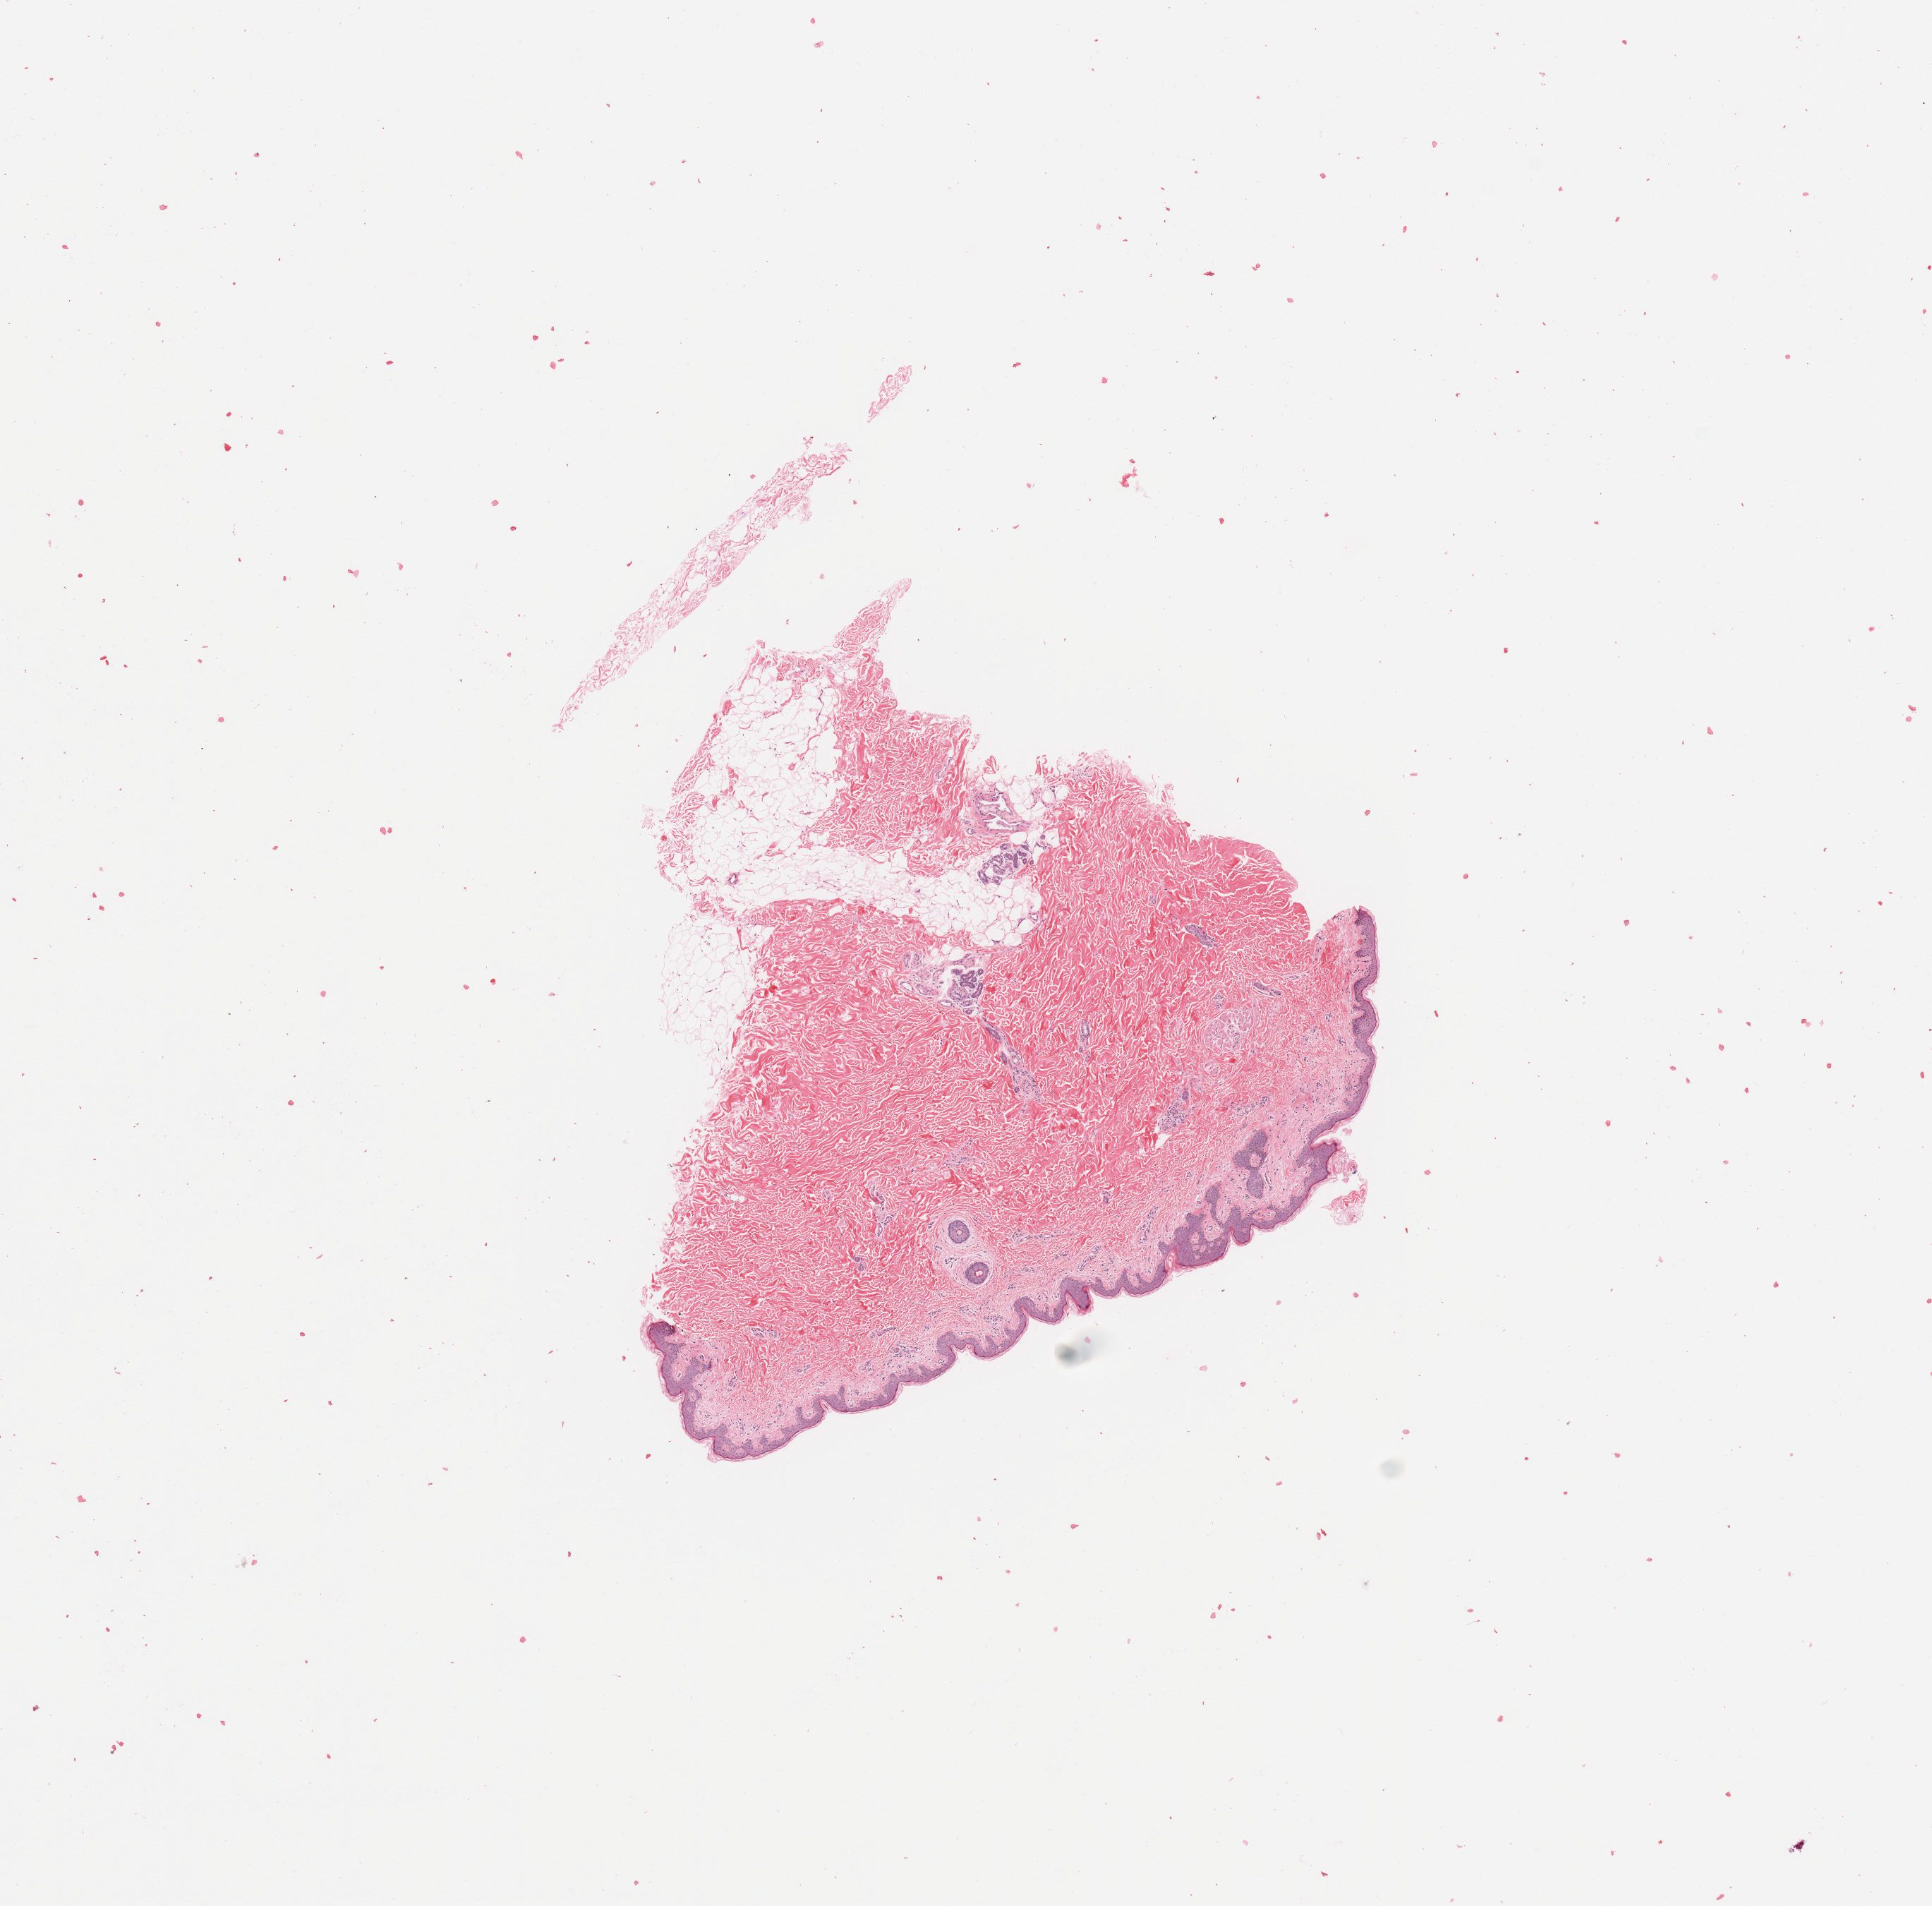
Whole-slide histology image, H&E-stained — shown as a low-resolution overview of the whole scanned area (about 10.8 x 10.7 mm, from a 20x scan), normal (non-tumour) tissue (melanoma cohort); sampled site not recorded. Patient: female, age 49 years.
- this section: normal (non-tumour) tissue from the same patient
- patient diagnosis: Malignant melanoma, NOS